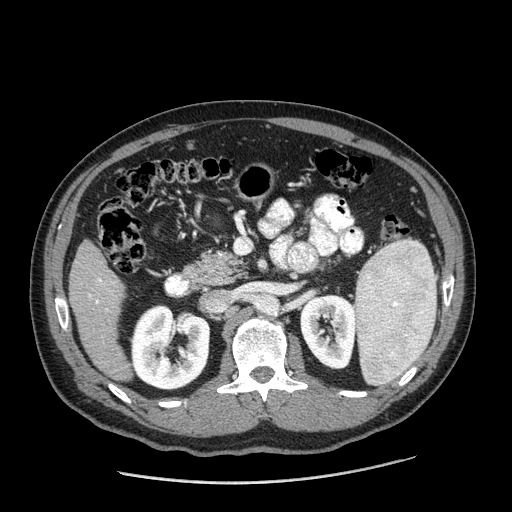
Contrast-enhanced abdominal CT (liver protocol), one axial slice. Position 71 of 198 along the scan axis. 120 kVp. One of 2 acquisitions stored at this slice position. Soft-tissue window (W 400 / L 40 HU). 2.5 mm slice thickness. 512 × 512 image matrix, field of view 400 × 400 mm. Case-level facts recorded for this patient, not image findings: diagnosis: hepatocellular carcinoma (patient treated with transarterial chemoembolisation; whether this scan precedes or follows treatment is not stated here); TNM stage (as recorded): Stage-II; Child-Pugh class: A; tumour nodularity: multinodular.
Annotated regions visible in this slice (semi-automatically segmented with operator editing):
- liver parenchyma outside the tumour (the mass and vessels are separate outlines, so this box may not span the whole liver): bounding box (x1, y1, x2, y2) in pixels: (68, 240, 132, 380)
- liver vessels: (96, 278, 102, 303)